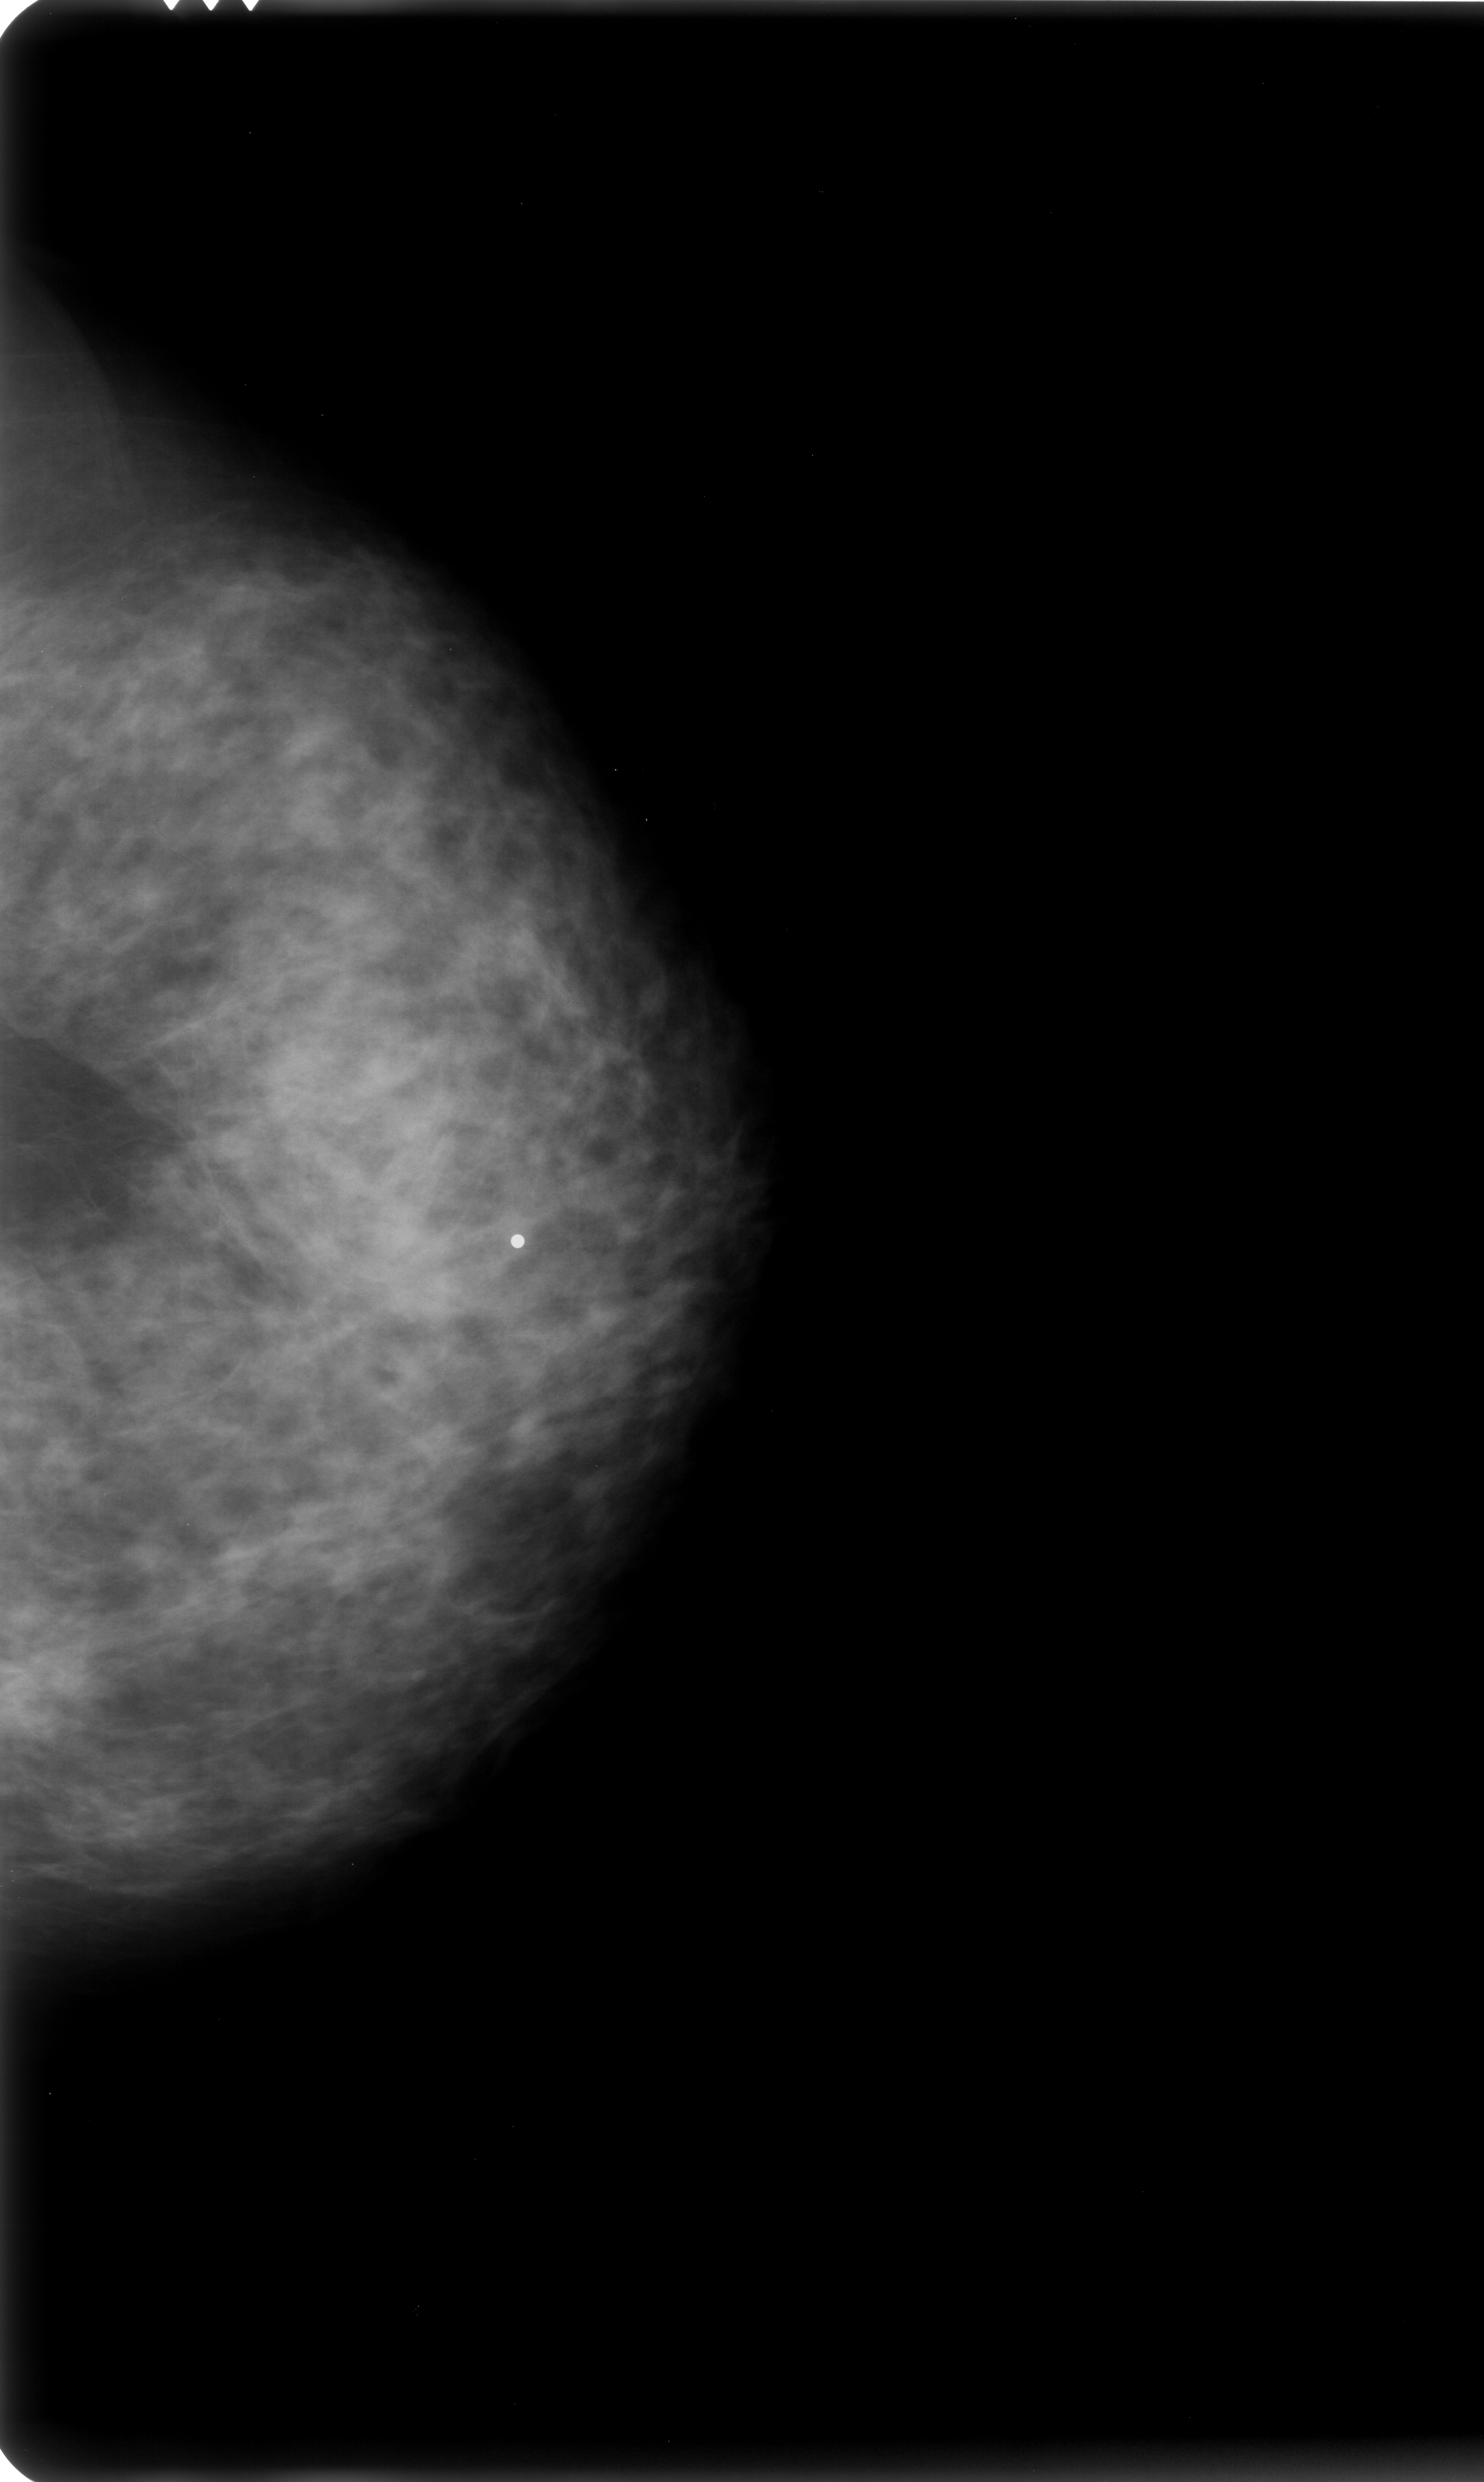
Mammogram (digitized film), left breast, craniocaudal (CC) view, BI-RADS breast density category 3 (scale 1–4).
Radiologist-marked abnormalities on this image: mass, shape architectural distortion, margins ill defined; BI-RADS assessment category 4; subtlety rating 2 on a 1 (subtle) to 5 (obvious) scale; pathology (as recorded): malignant.